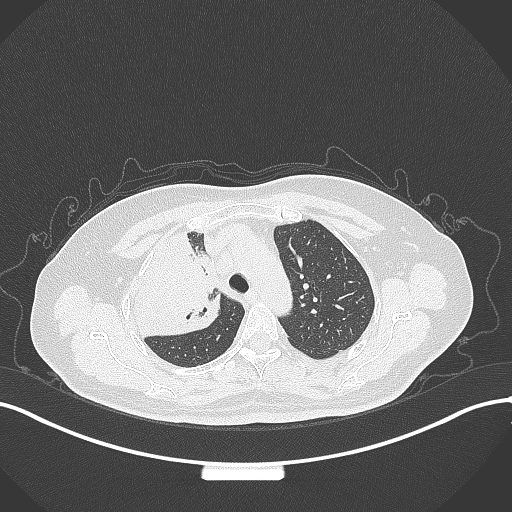
Chest CT, one axial slice; position 237 of 309 along the scan axis; 120 kVp; lung window (W 1500 / L -600 HU); 1 mm slice thickness; 512 × 512 image matrix, field of view 400 × 400 mm. Patient: female, 60 years. Case-level facts recorded for this patient, not image findings: clinical TNM (as recorded): T3 N1 M1.
Structures marked on this image (rectangle marked by the reading radiologist):
- lung tumour (recorded histology: adenocarcinoma): box from (x=132, y=232) to (x=225, y=336) px